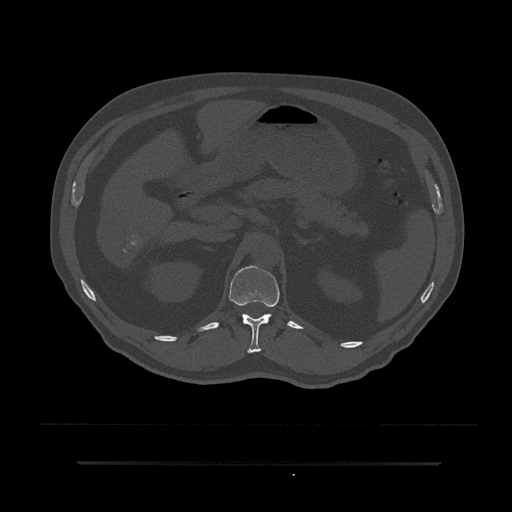
CT including the spine, one axial slice. Slice 199 of 797 in the series (ordered by position). Reconstruction kernel Br40s/3. 120 kVp. Bone window (W 1800 / L 400 HU). 0.5 mm slice thickness. 512 × 512 image matrix, field of view 464 × 464 mm. Male patient, age 59 years. Case-level facts recorded for this patient, not image findings: primary cancer: bile ducts; vertebrae with lytic lesions (as recorded): T10.
Structures marked on this image (semi-automatically segmented with operator editing):
- T12 vertebra: box from (x=229, y=266) to (x=280, y=354) px